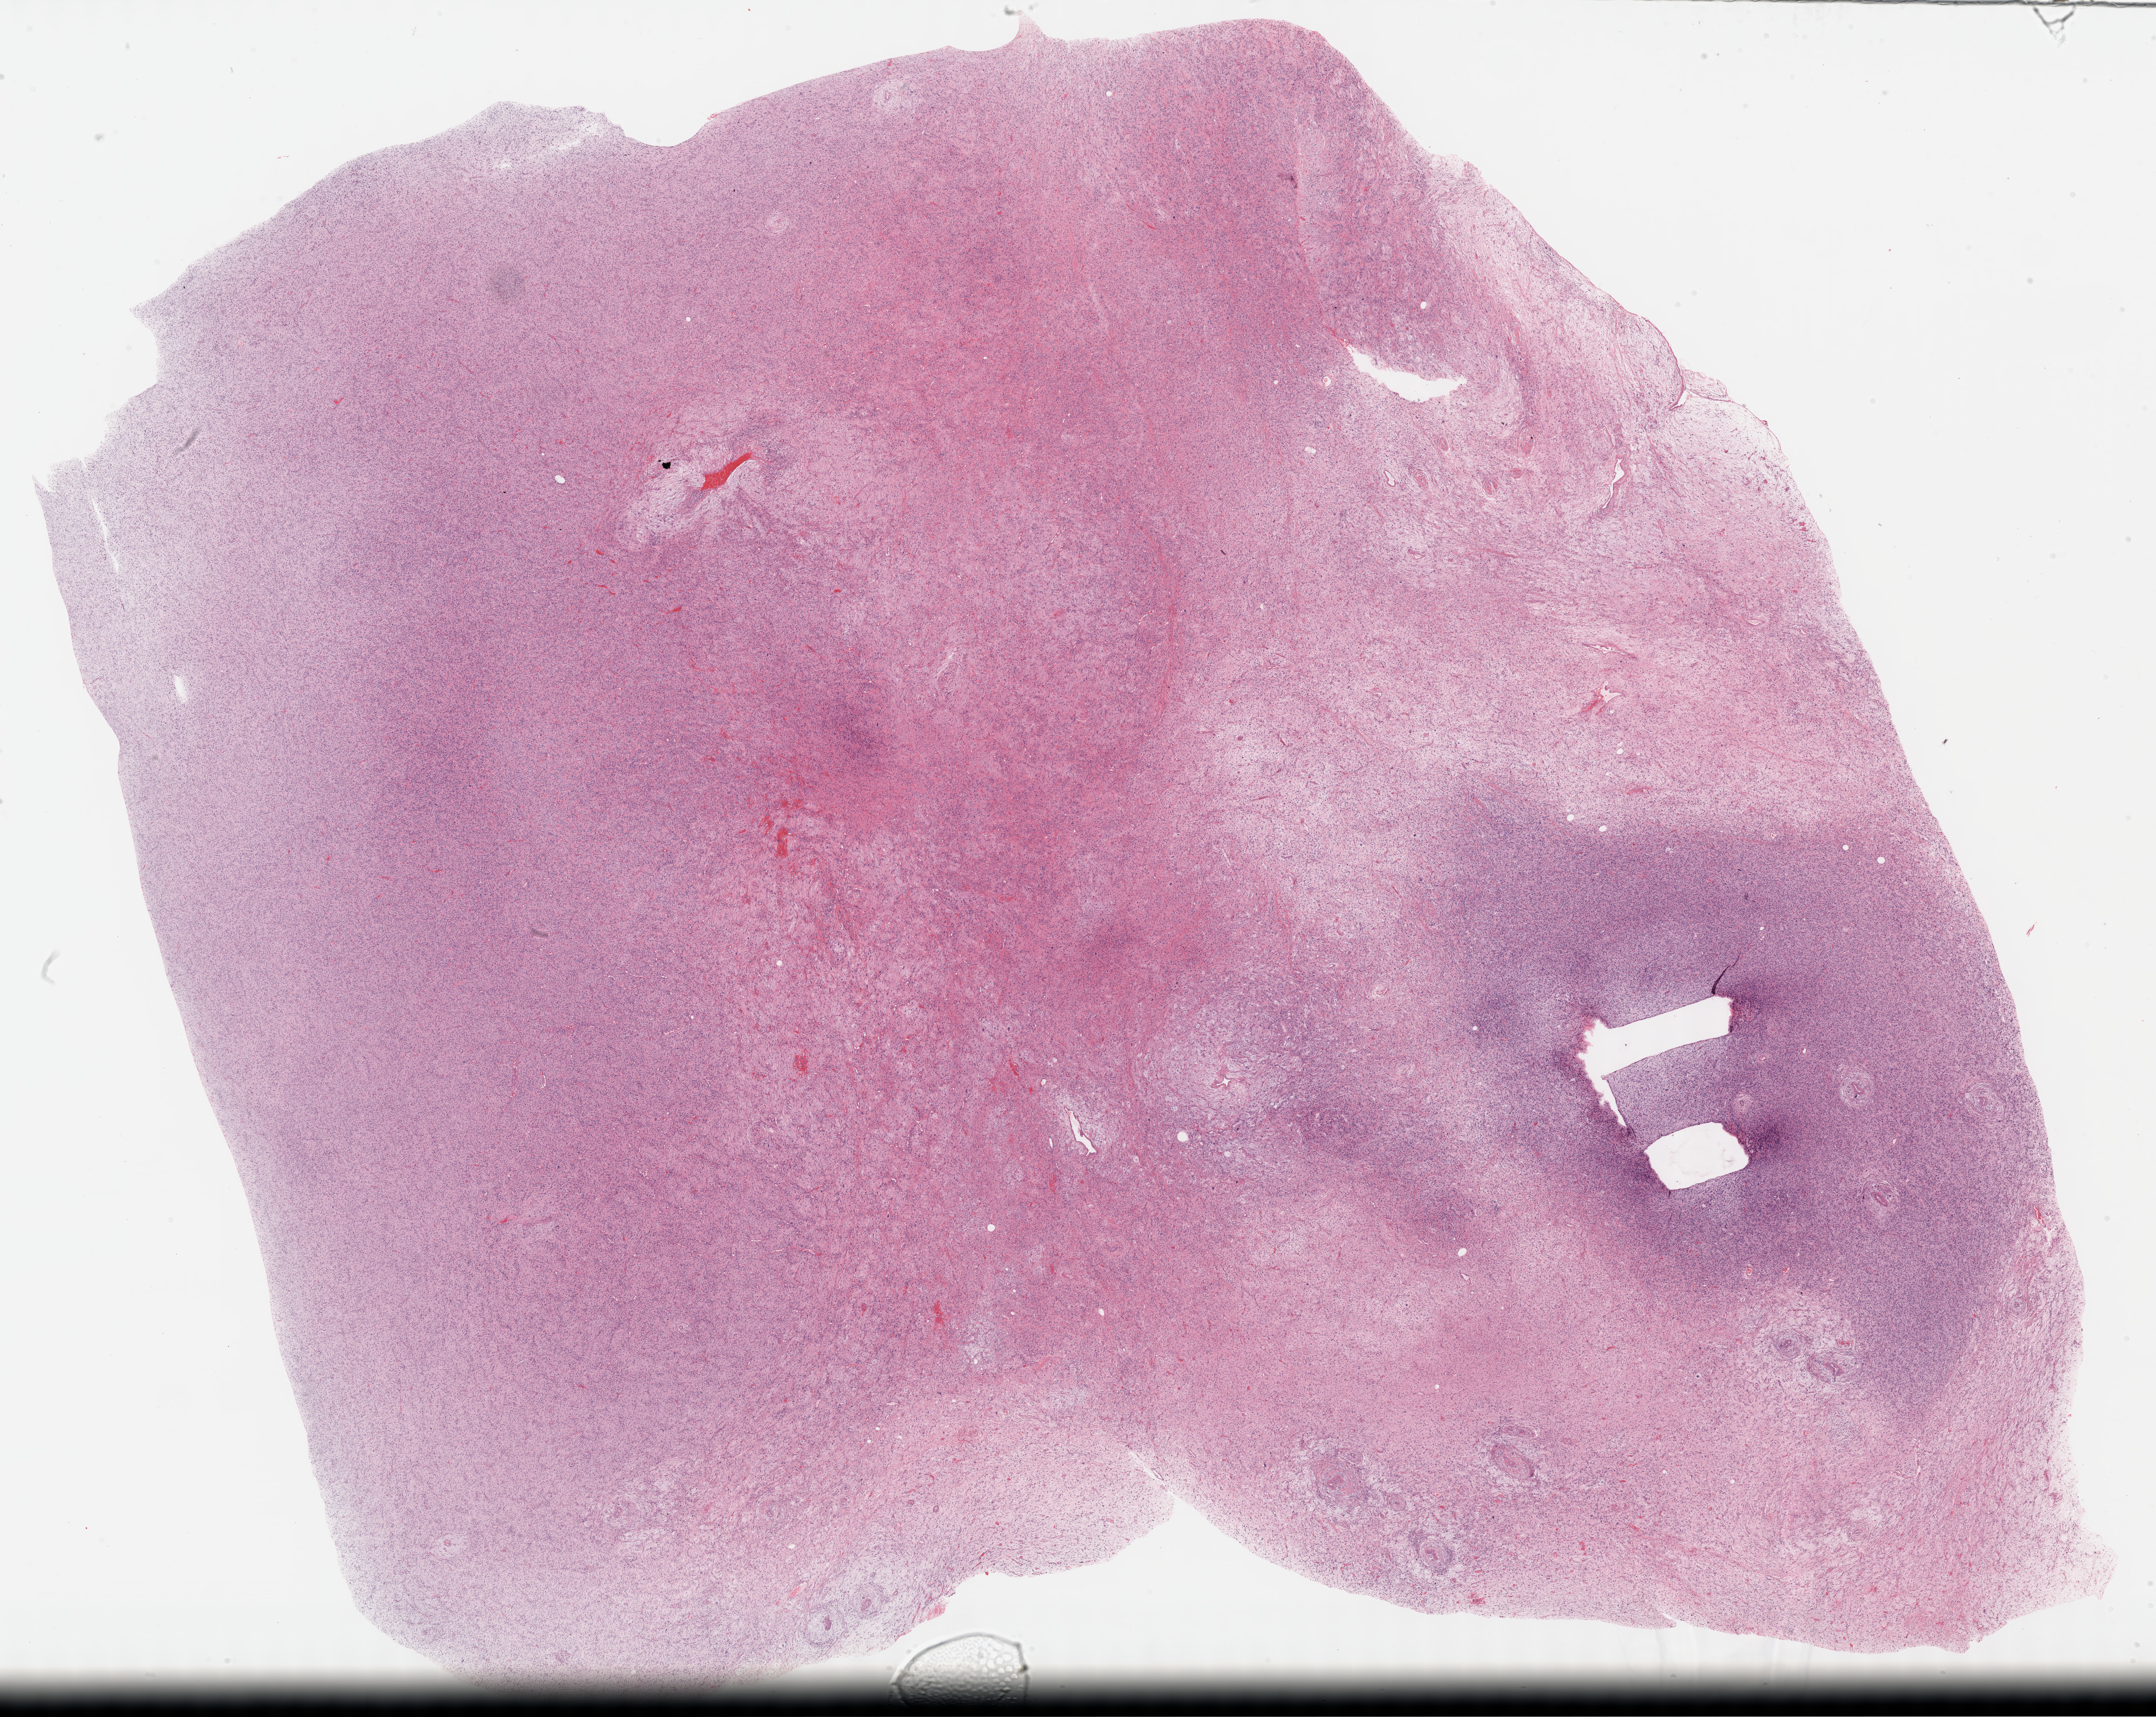
Digitized Hematoxylin and eosin (H&E) stained tissue section (whole slide), shown as a low-resolution overview of the whole scanned area (about 29.7 x 23.7 mm), formalin-fixed paraffin-embedded (FFPE) diagnostic section, sample: primary tumour, retroperitoneum and peritoneum. Male patient; age at initial diagnosis 43 years.
Diagnosis: Dedifferentiated liposarcoma (retroperitoneum).